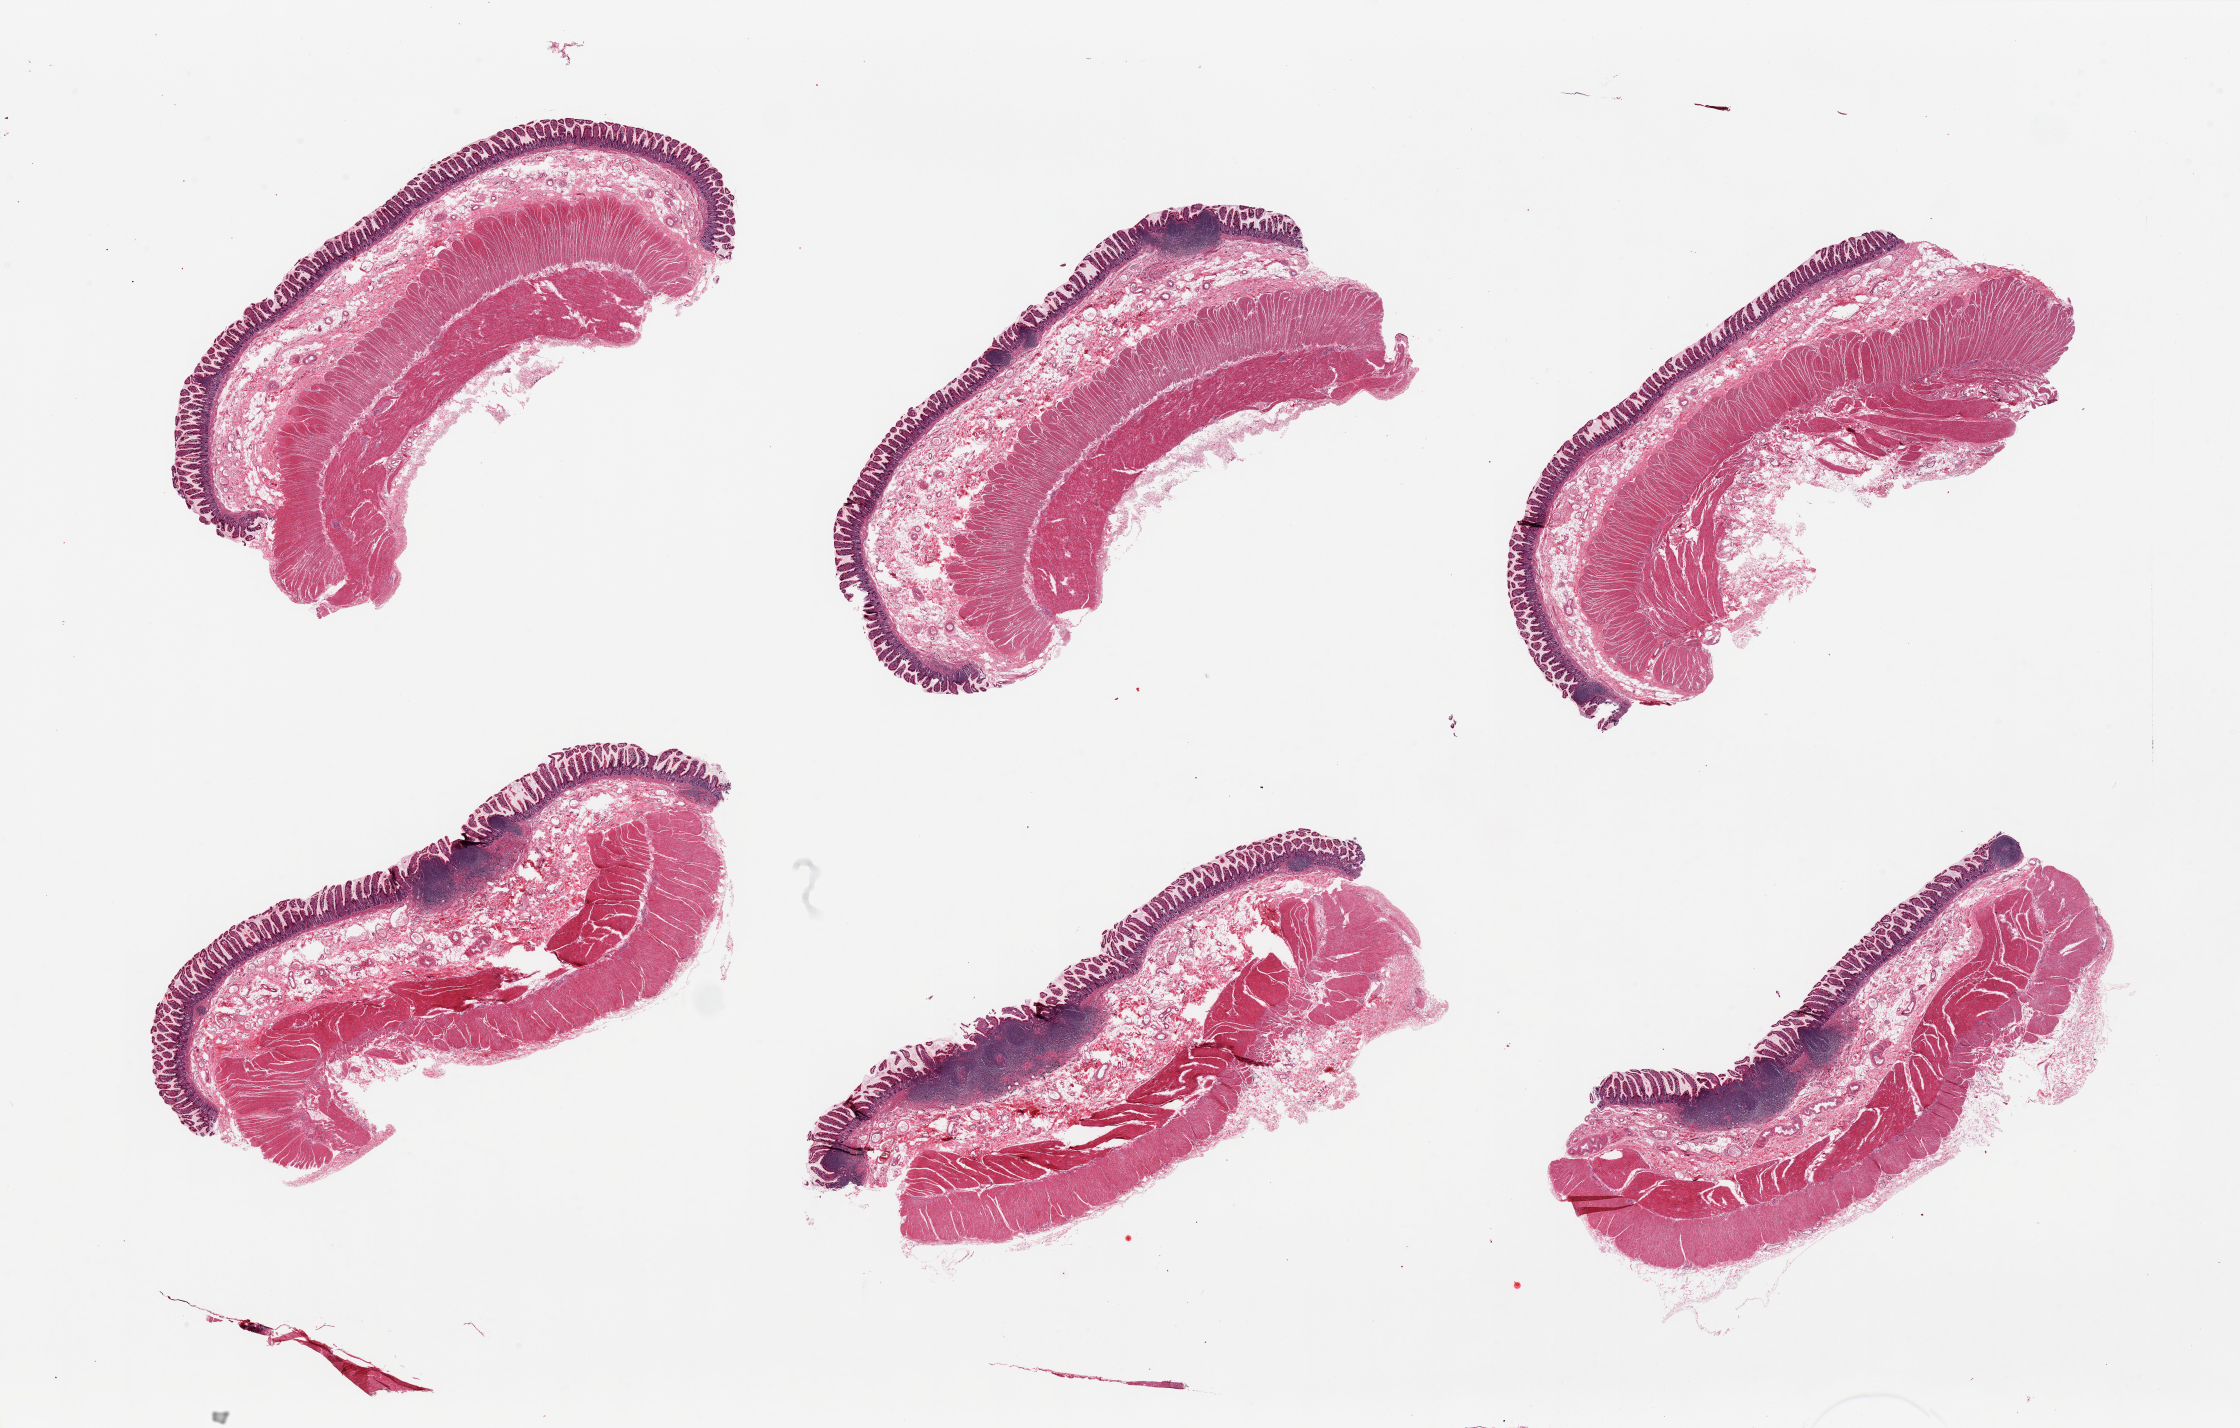
Digitized haematoxylin and eosin-stained section, whole scanned area (about 35.4 x 22.6 mm) shown as a low-resolution overview, PAXgene-fixed paraffin-embedded (PFPE) section, sampled site (target tissue): ileum, donor tissue sample. Donor sex: male.
• pathologist's review note for this sample: 6 pieces; Several mucosal lymphoid deposits; Muscularis propria makes up 80% of pieces; It should be dissected off the ileal aliquots